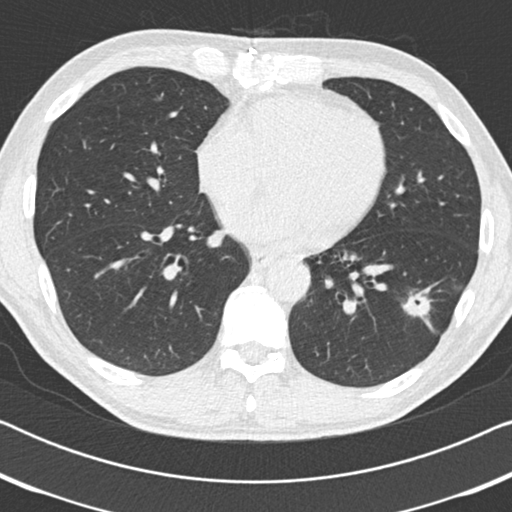
Axial slice from a low-dose chest CT screening exam. Third screening round (two years after baseline). Lung window (W 1500 / L -600 HU). 512 × 512 image matrix, field of view 330 × 330 mm. Male participant, aged 59 years at enrolment.
Lesion marked by an expert reader, bounding box <389,276,456,339> (left, top, right, bottom; pixels). The screening reader recorded 2 non-calcified nodules or masses ≥4 mm on this exam (left lower lobe, right middle lobe); which of them this box marks is not recorded. Participant outcome: lung cancer diagnosed 73 days after this screen — adenocarcinoma, NOS, left lower lobe, poorly differentiated (G3), stage IA (AJCC 6th edition), 20 mm at pathology.